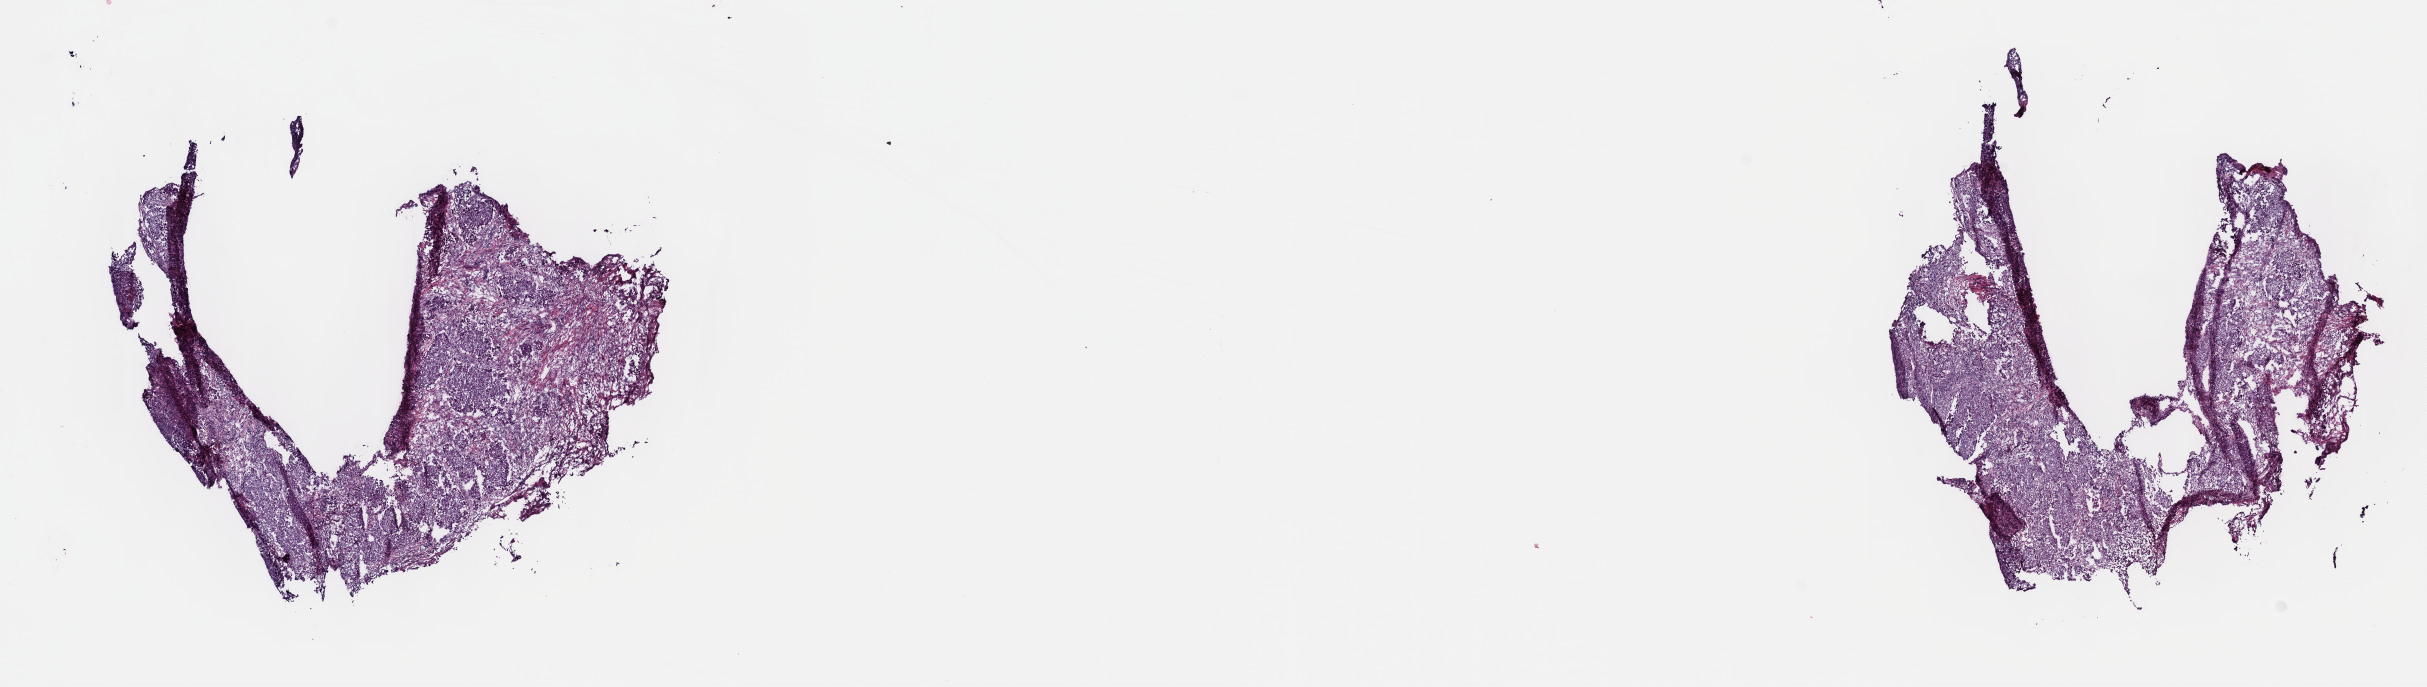
Hematoxylin and eosin (H&E) stained whole-slide image, whole scanned area (about 19.6 x 5.6 mm, slide scanned at 40x) shown as a low-resolution overview. Frozen section. Bladder, primary tumour sample. Patient: male, age at initial diagnosis 72 years. Histologic grade: high grade. Pathologist review of this section (percent, as recorded): tumour cells 80%, tumour nuclei 80%, normal cells 0%, stromal cells 20%, necrosis 0%. Inflammatory infiltration, as recorded: lymphocyte infiltration 2%, monocyte infiltration 1%, neutrophil infiltration 5%.
Pathologic diagnosis: Transitional cell carcinoma. AJCC pathologic stage: II (7th edition).